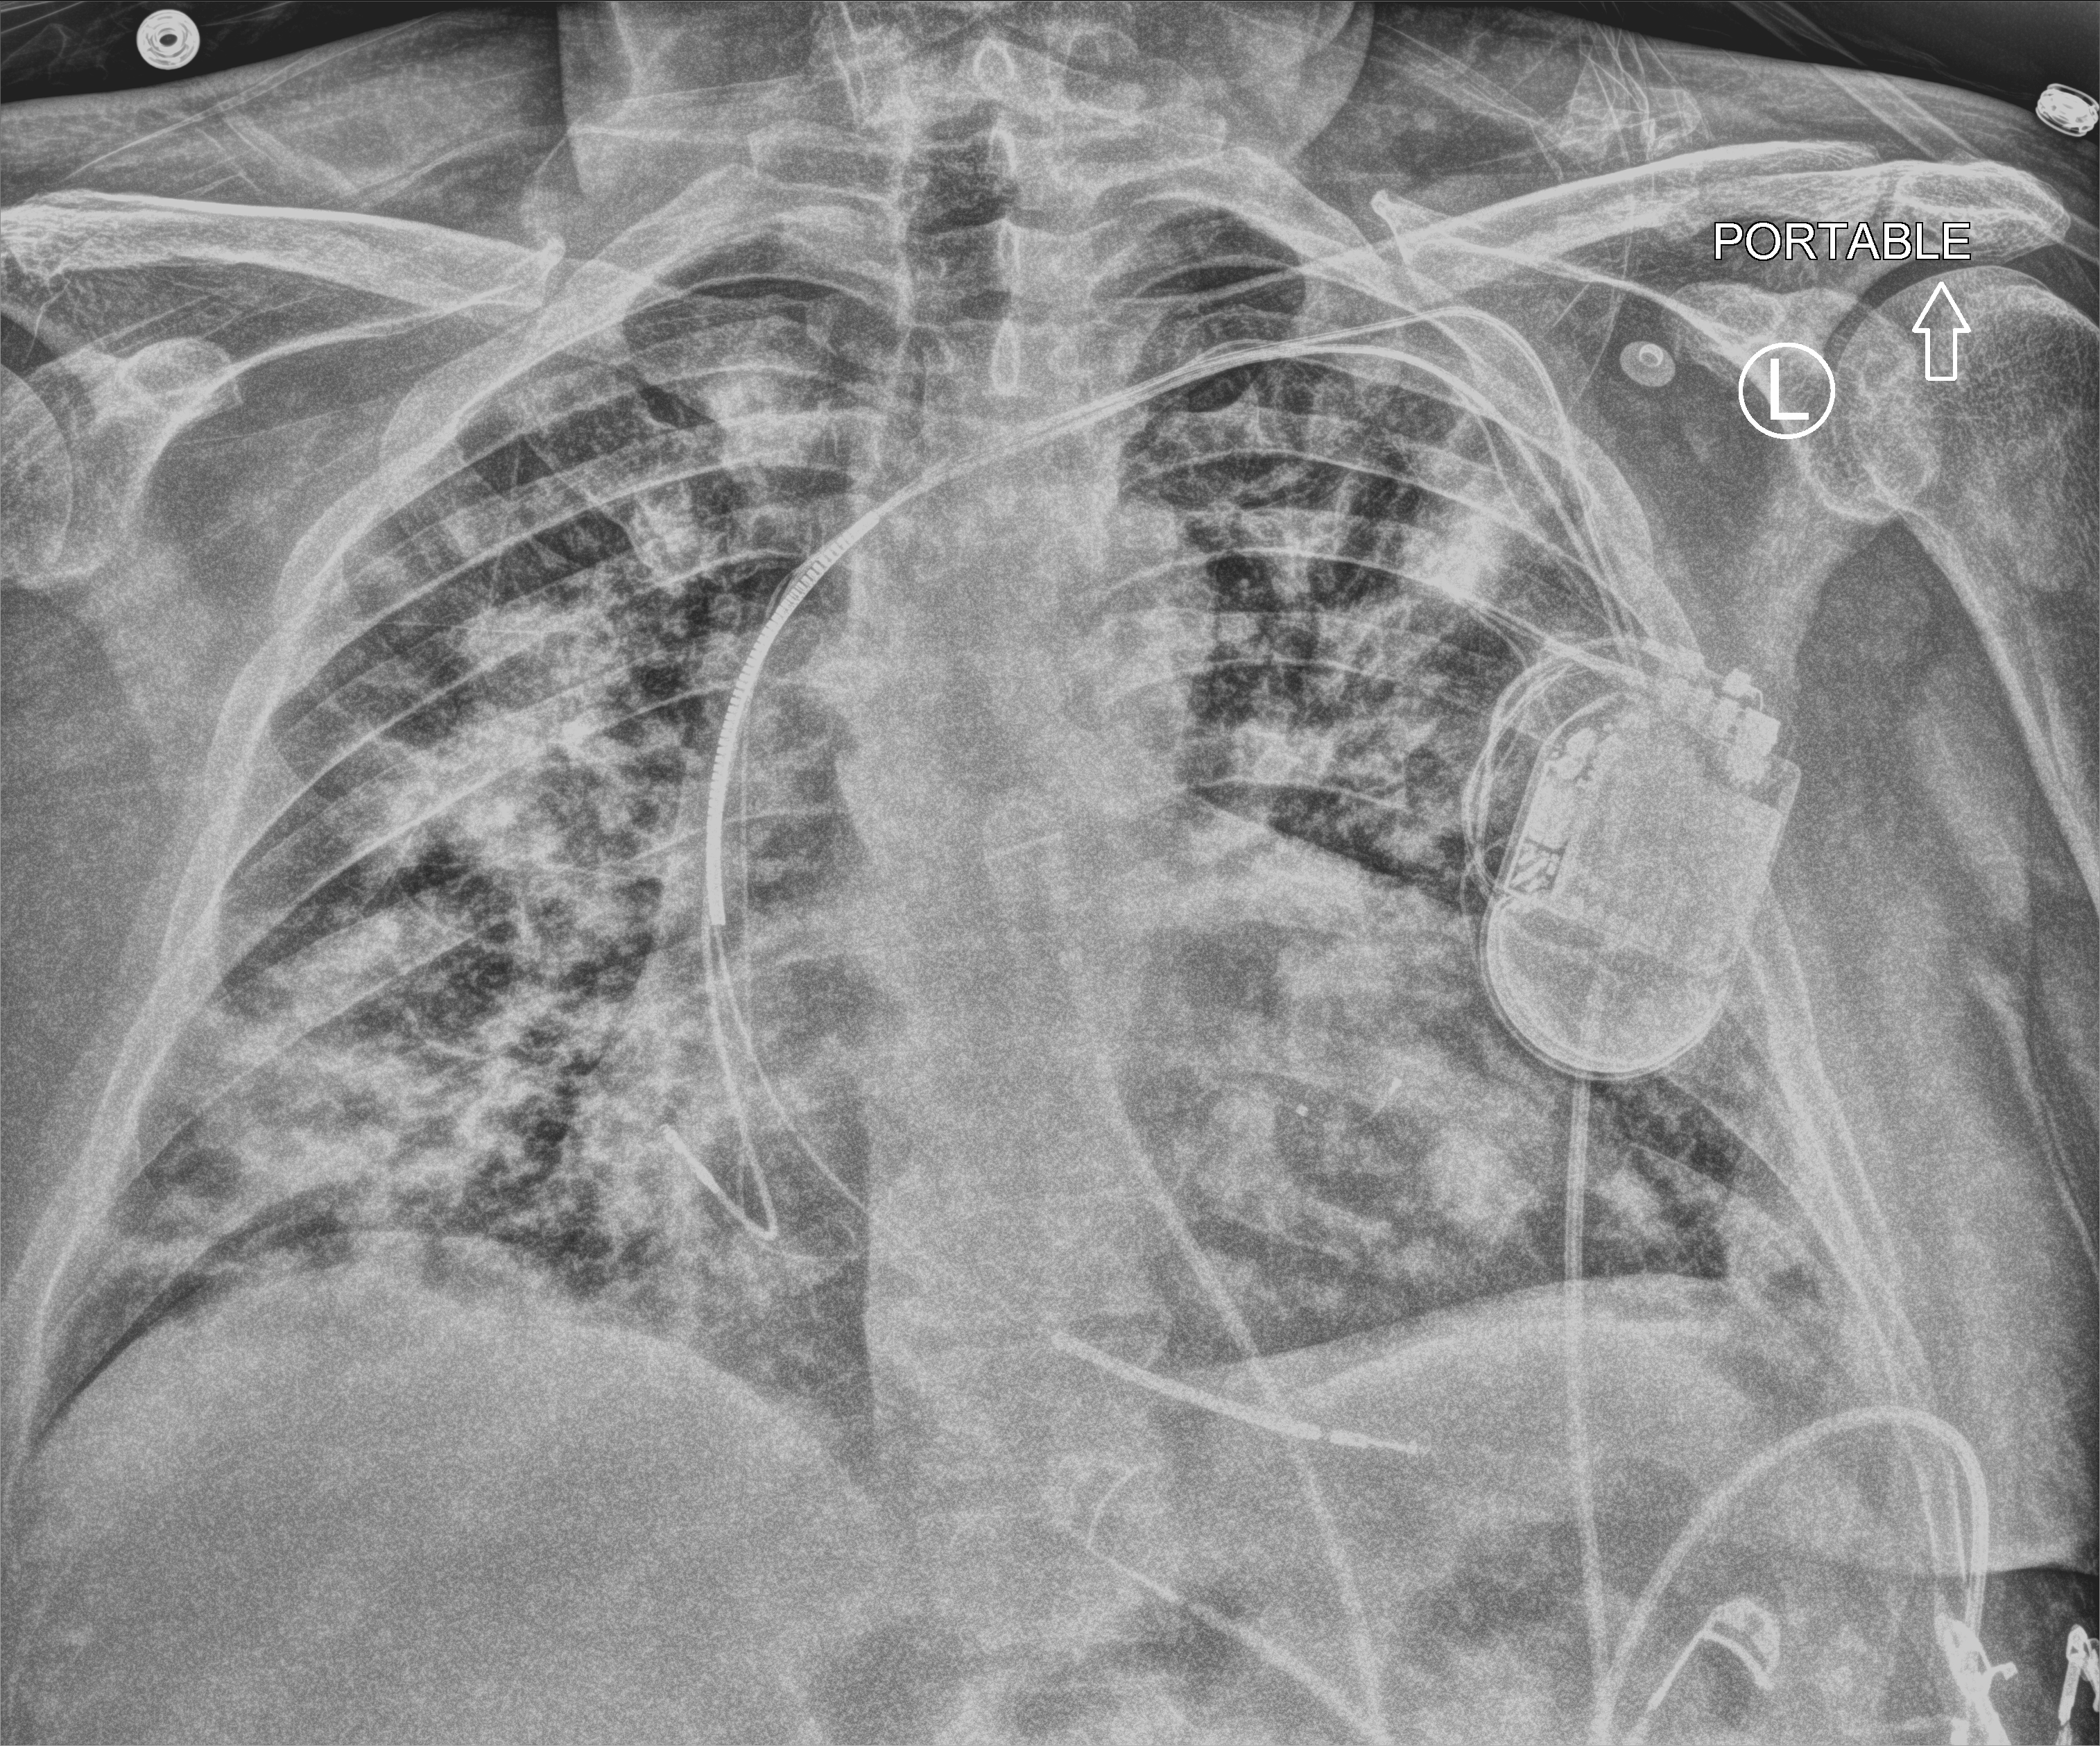
Portable chest radiograph. Patient hospitalised with COVID-19; male, aged 60–74 years.
Admission-level facts for this patient (not findings on this image; timing relative to this image not recorded):
- length of hospital stay: 27 days
- mechanically ventilated during this hospital stay: no